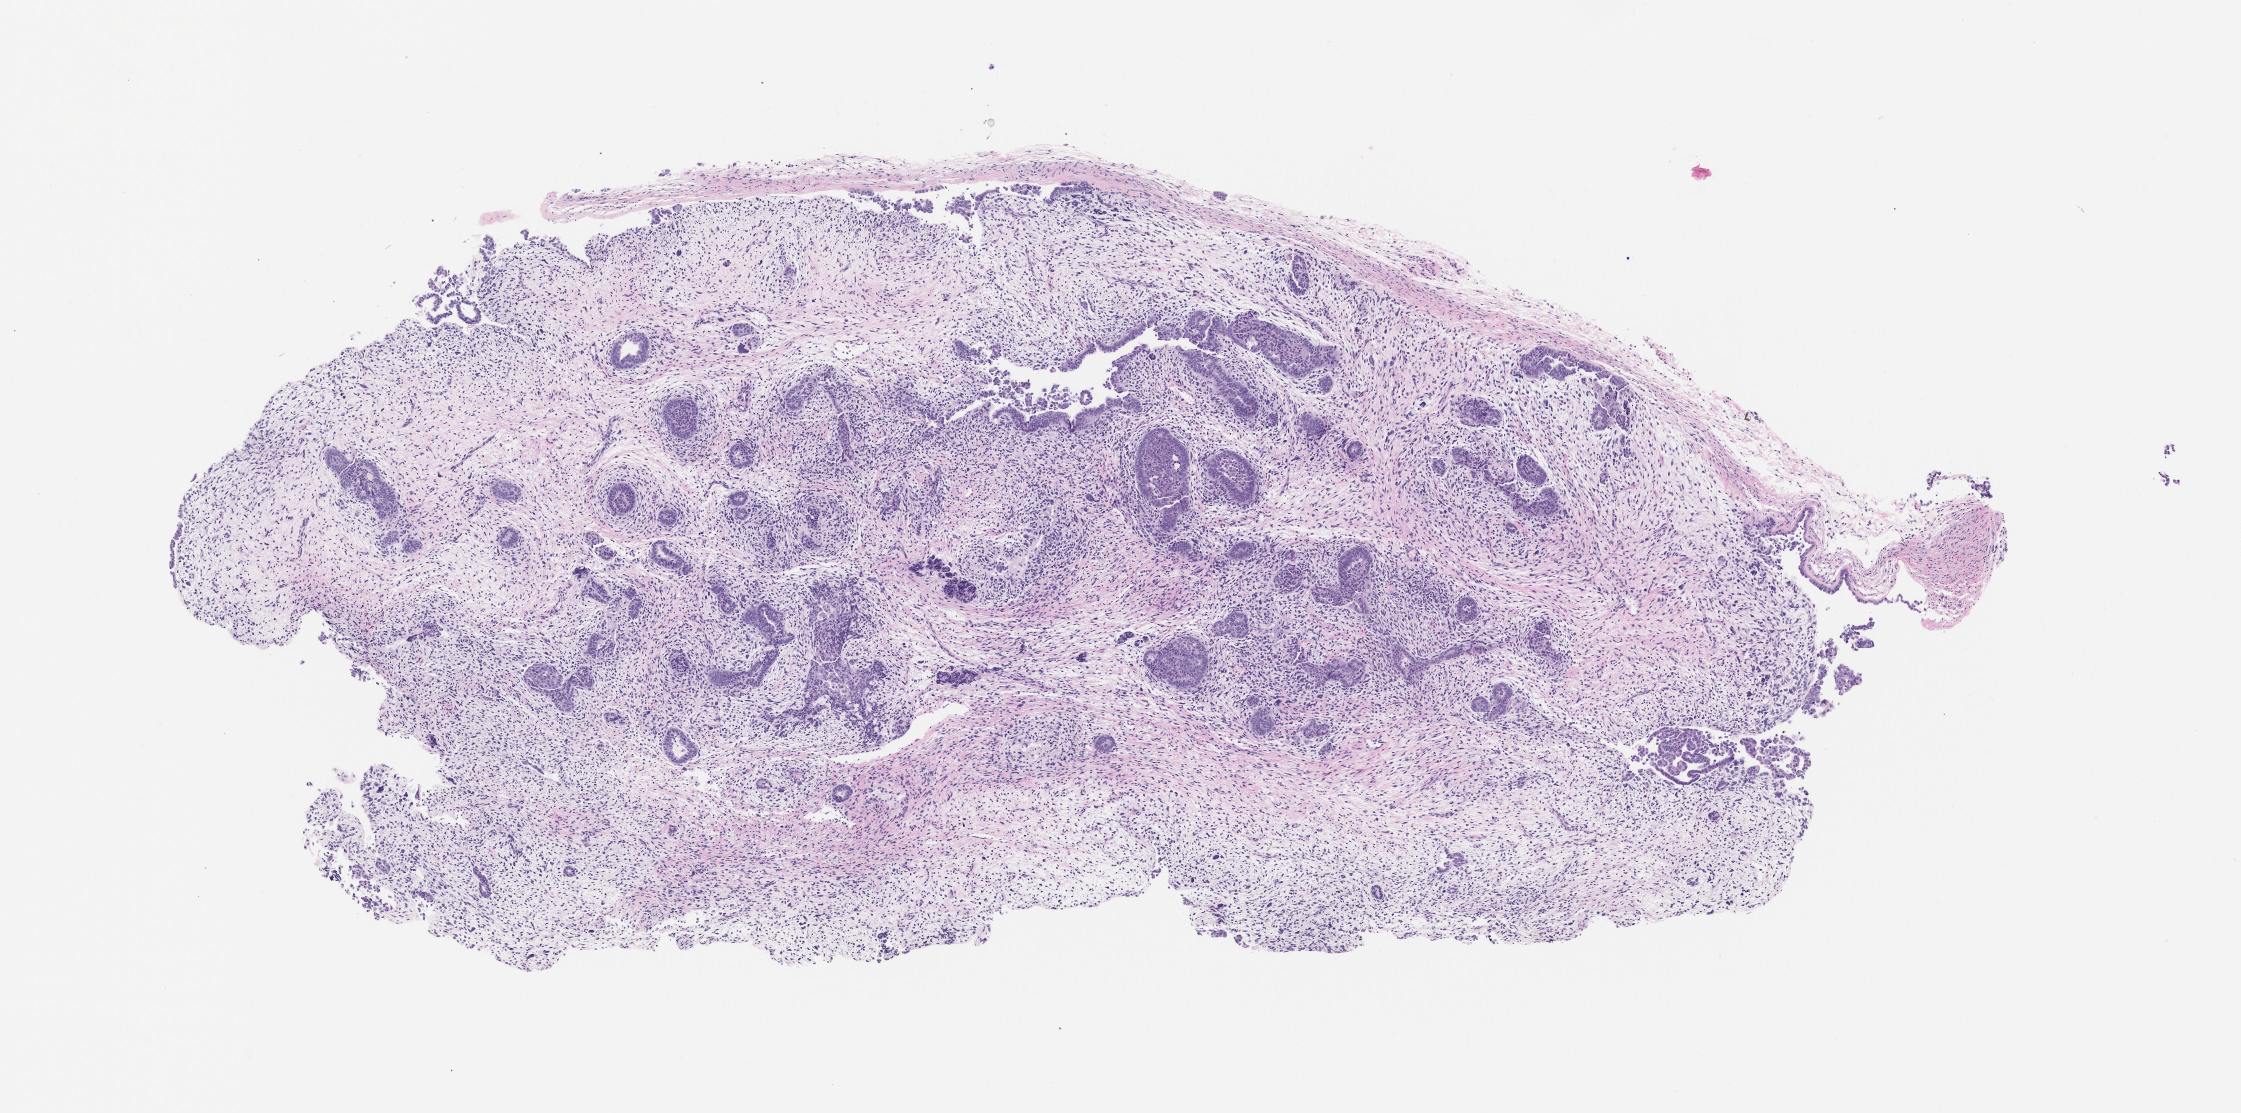
Whole-slide image, H&E: patient-derived xenograft (human tumor grown in a mouse), shown as a low-resolution overview of the whole scanned area (about 9.0 x 4.5 mm); FFPE section; originating tumor site category: uterus.
- originating patient diagnosis: Carcinosarcoma